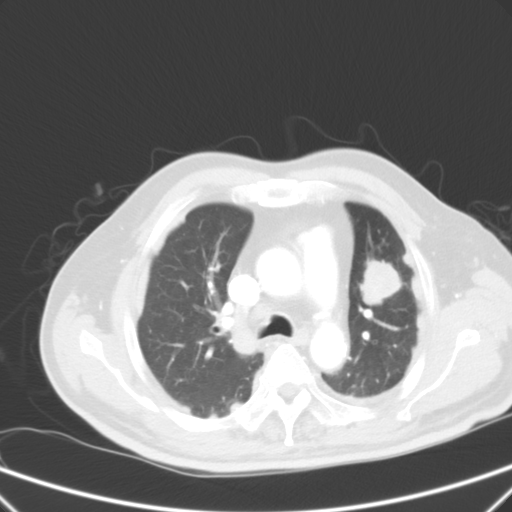
Chest CT, one axial slice. Position 41 of 59 along the scan axis. 120 kVp. Intravenous contrast given. Lung window (W 1500 / L -600 HU). 512 × 512 image matrix, field of view 357 × 357 mm. Patient: male, 66 years. From the clinical record (not read from this slice): clinical TNM (as recorded): T1c N3 M1a.
Annotated regions visible in this slice (bounding box drawn by a radiologist):
- lung tumour (recorded histology: squamous cell carcinoma): box from (x=358, y=257) to (x=408, y=314) px